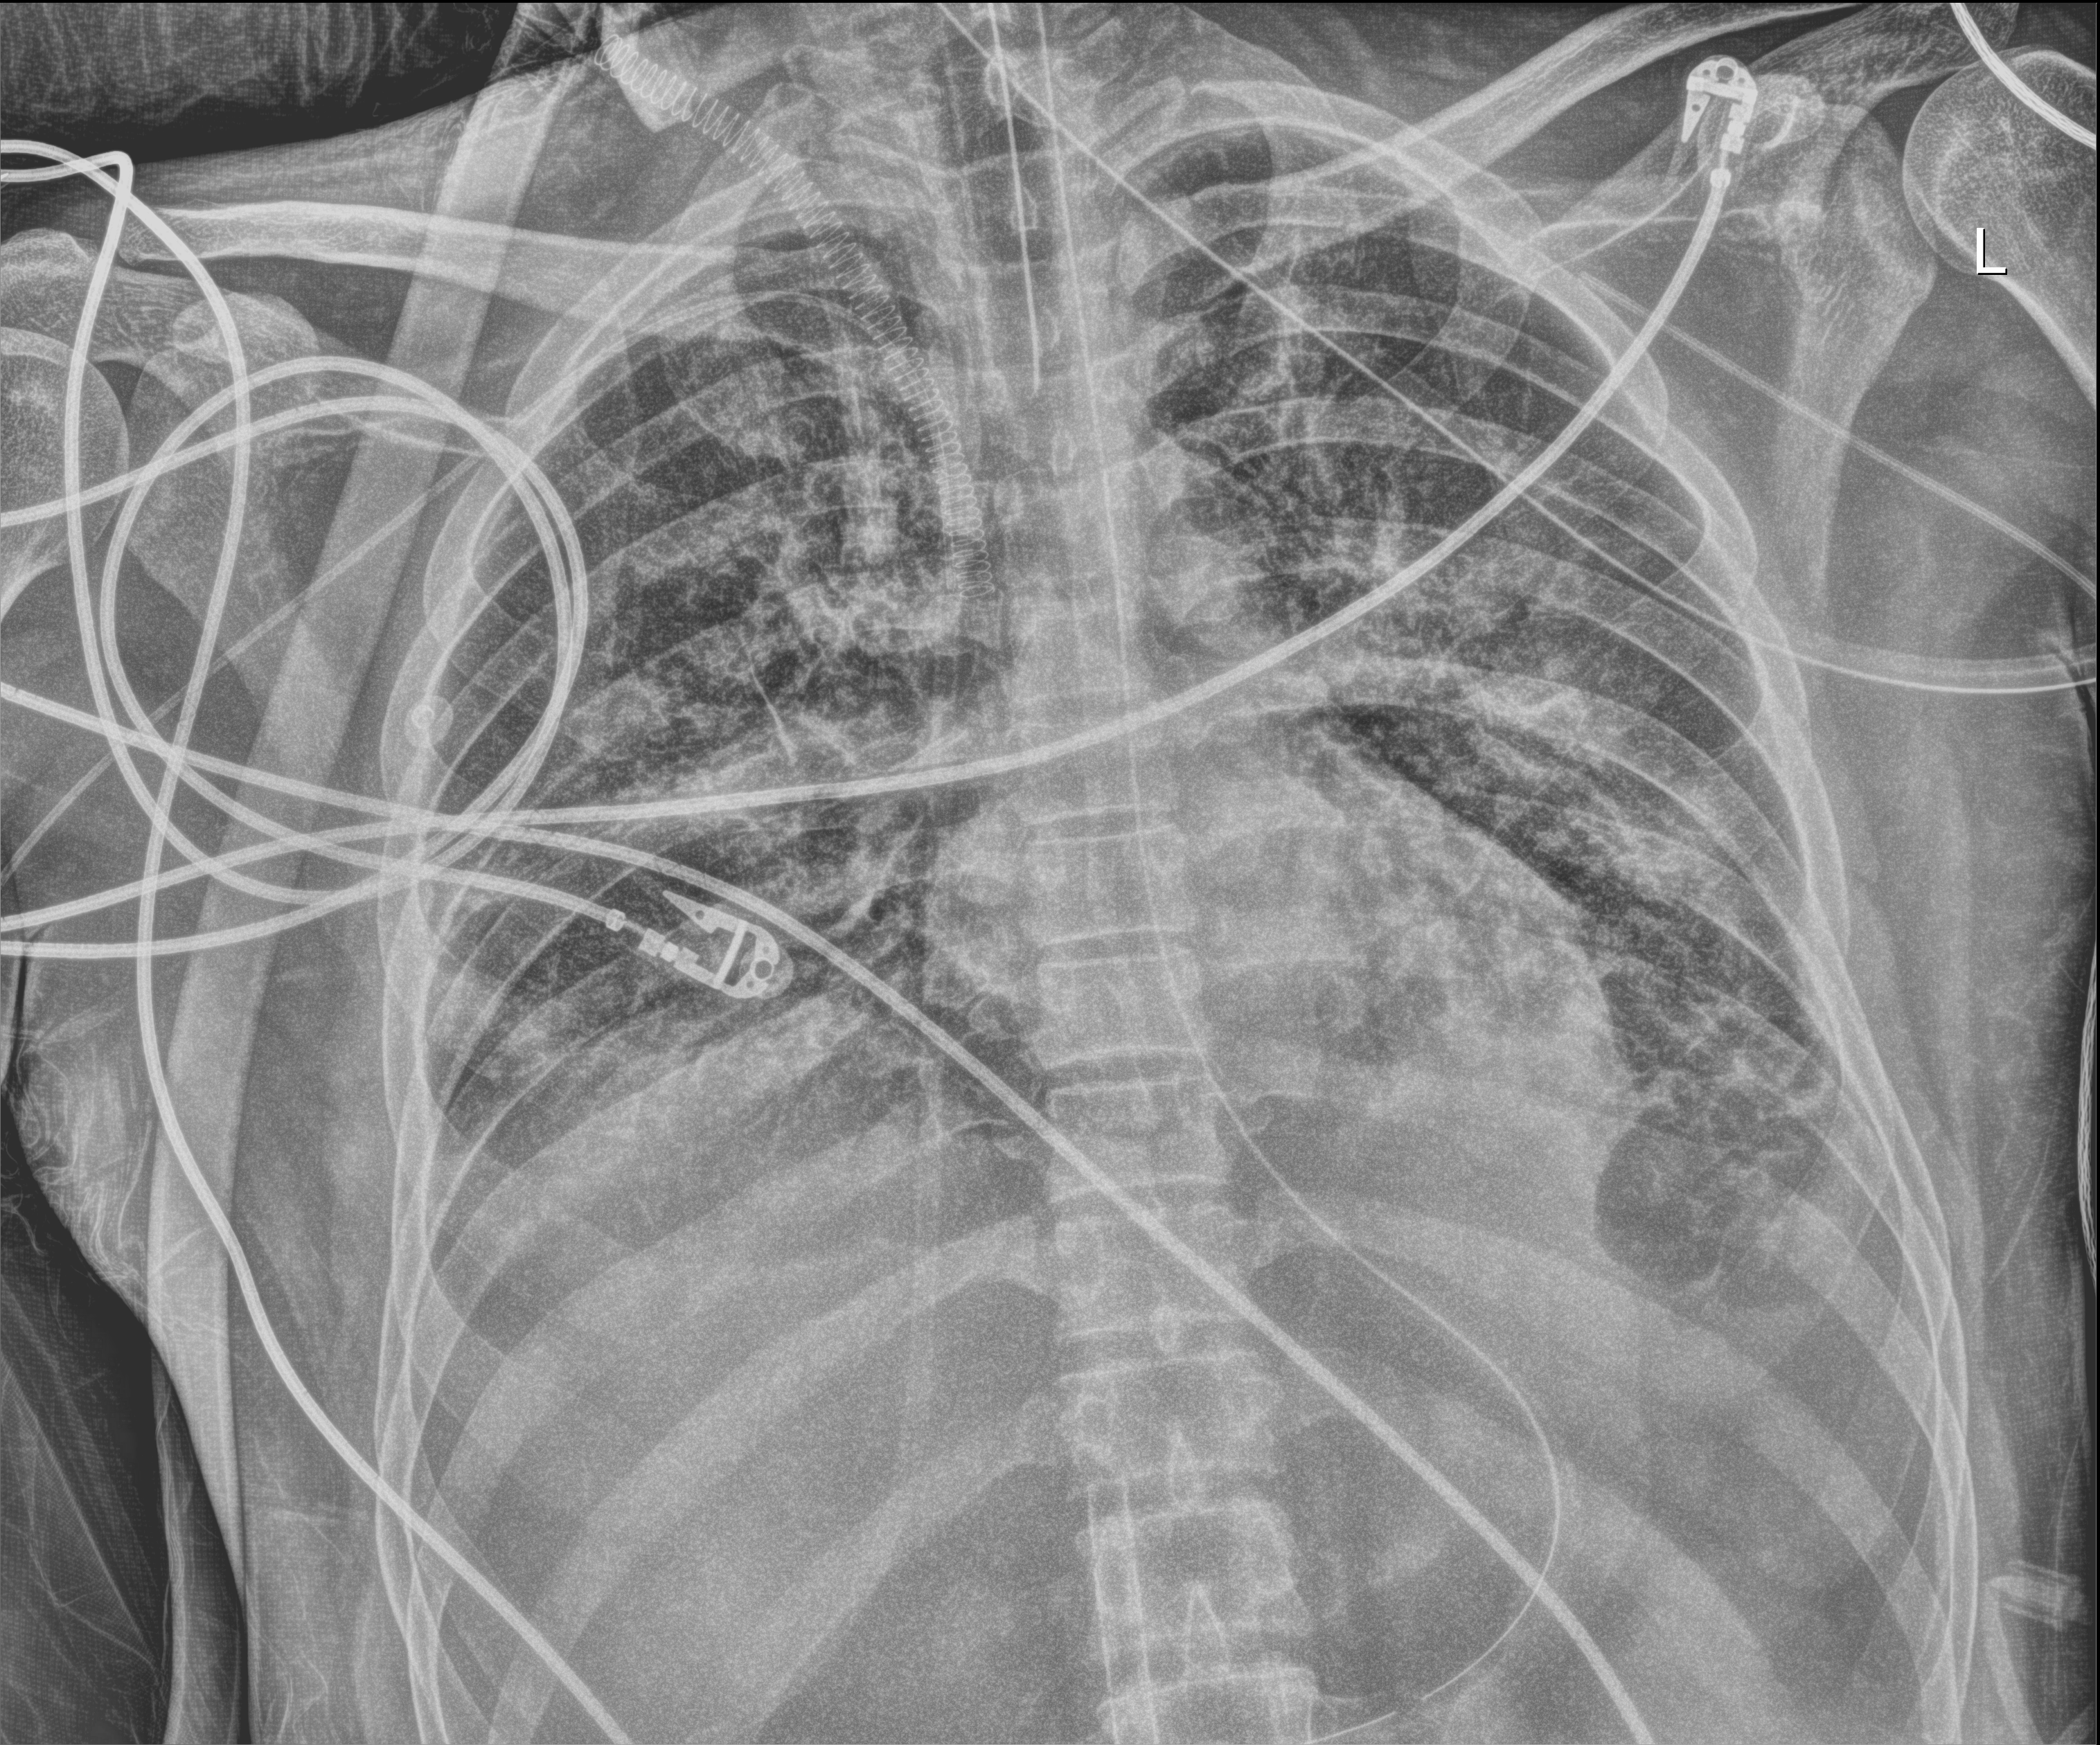
Chest X-ray (portable), anteroposterior (AP) projection. Patient hospitalised with COVID-19, aged 18–59 years.
Admission-level facts for this patient (not findings on this image; timing relative to this image not recorded):
- admitted to intensive care during this hospital stay: yes